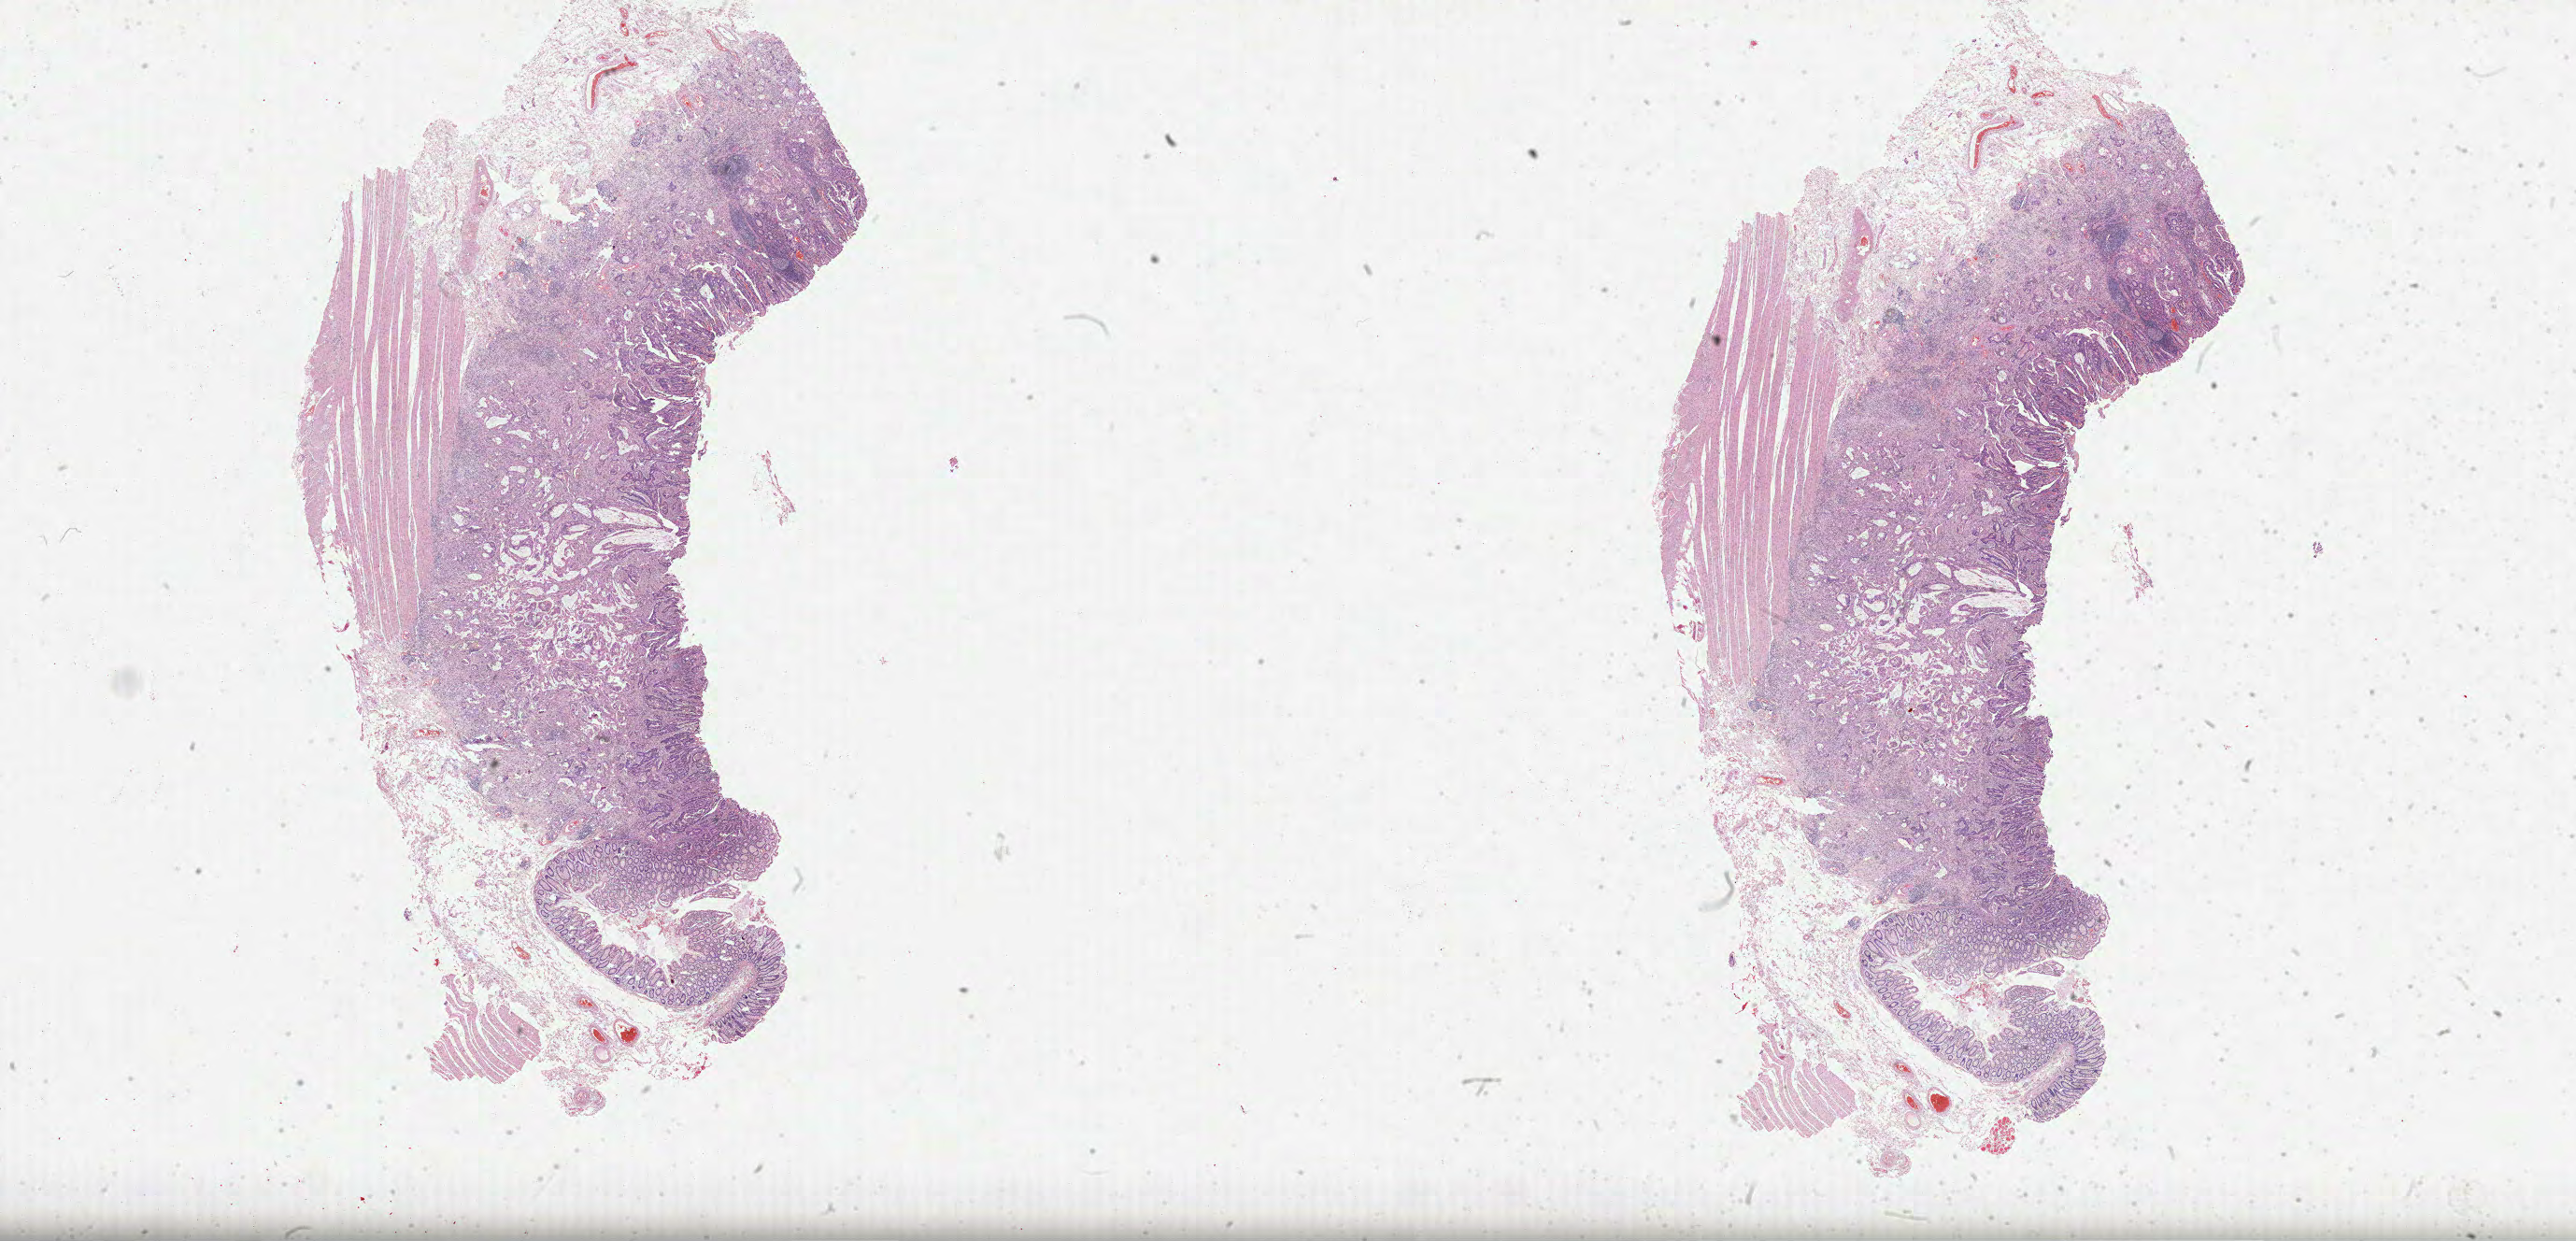
Digitized H&E-stained tissue section (whole slide) — shown as a low-resolution overview of the whole scanned area (about 44.5 x 21.4 mm, acquisition: 40x scan), FFPE section, sample: primary tumour, colon. Female patient; age at initial diagnosis 62 years.
Lymph nodes positive (case pathology): 0 of 22 examined. AJCC pathologic stage: IIA (7th edition). Pathologic diagnosis: Mucinous adenocarcinoma.